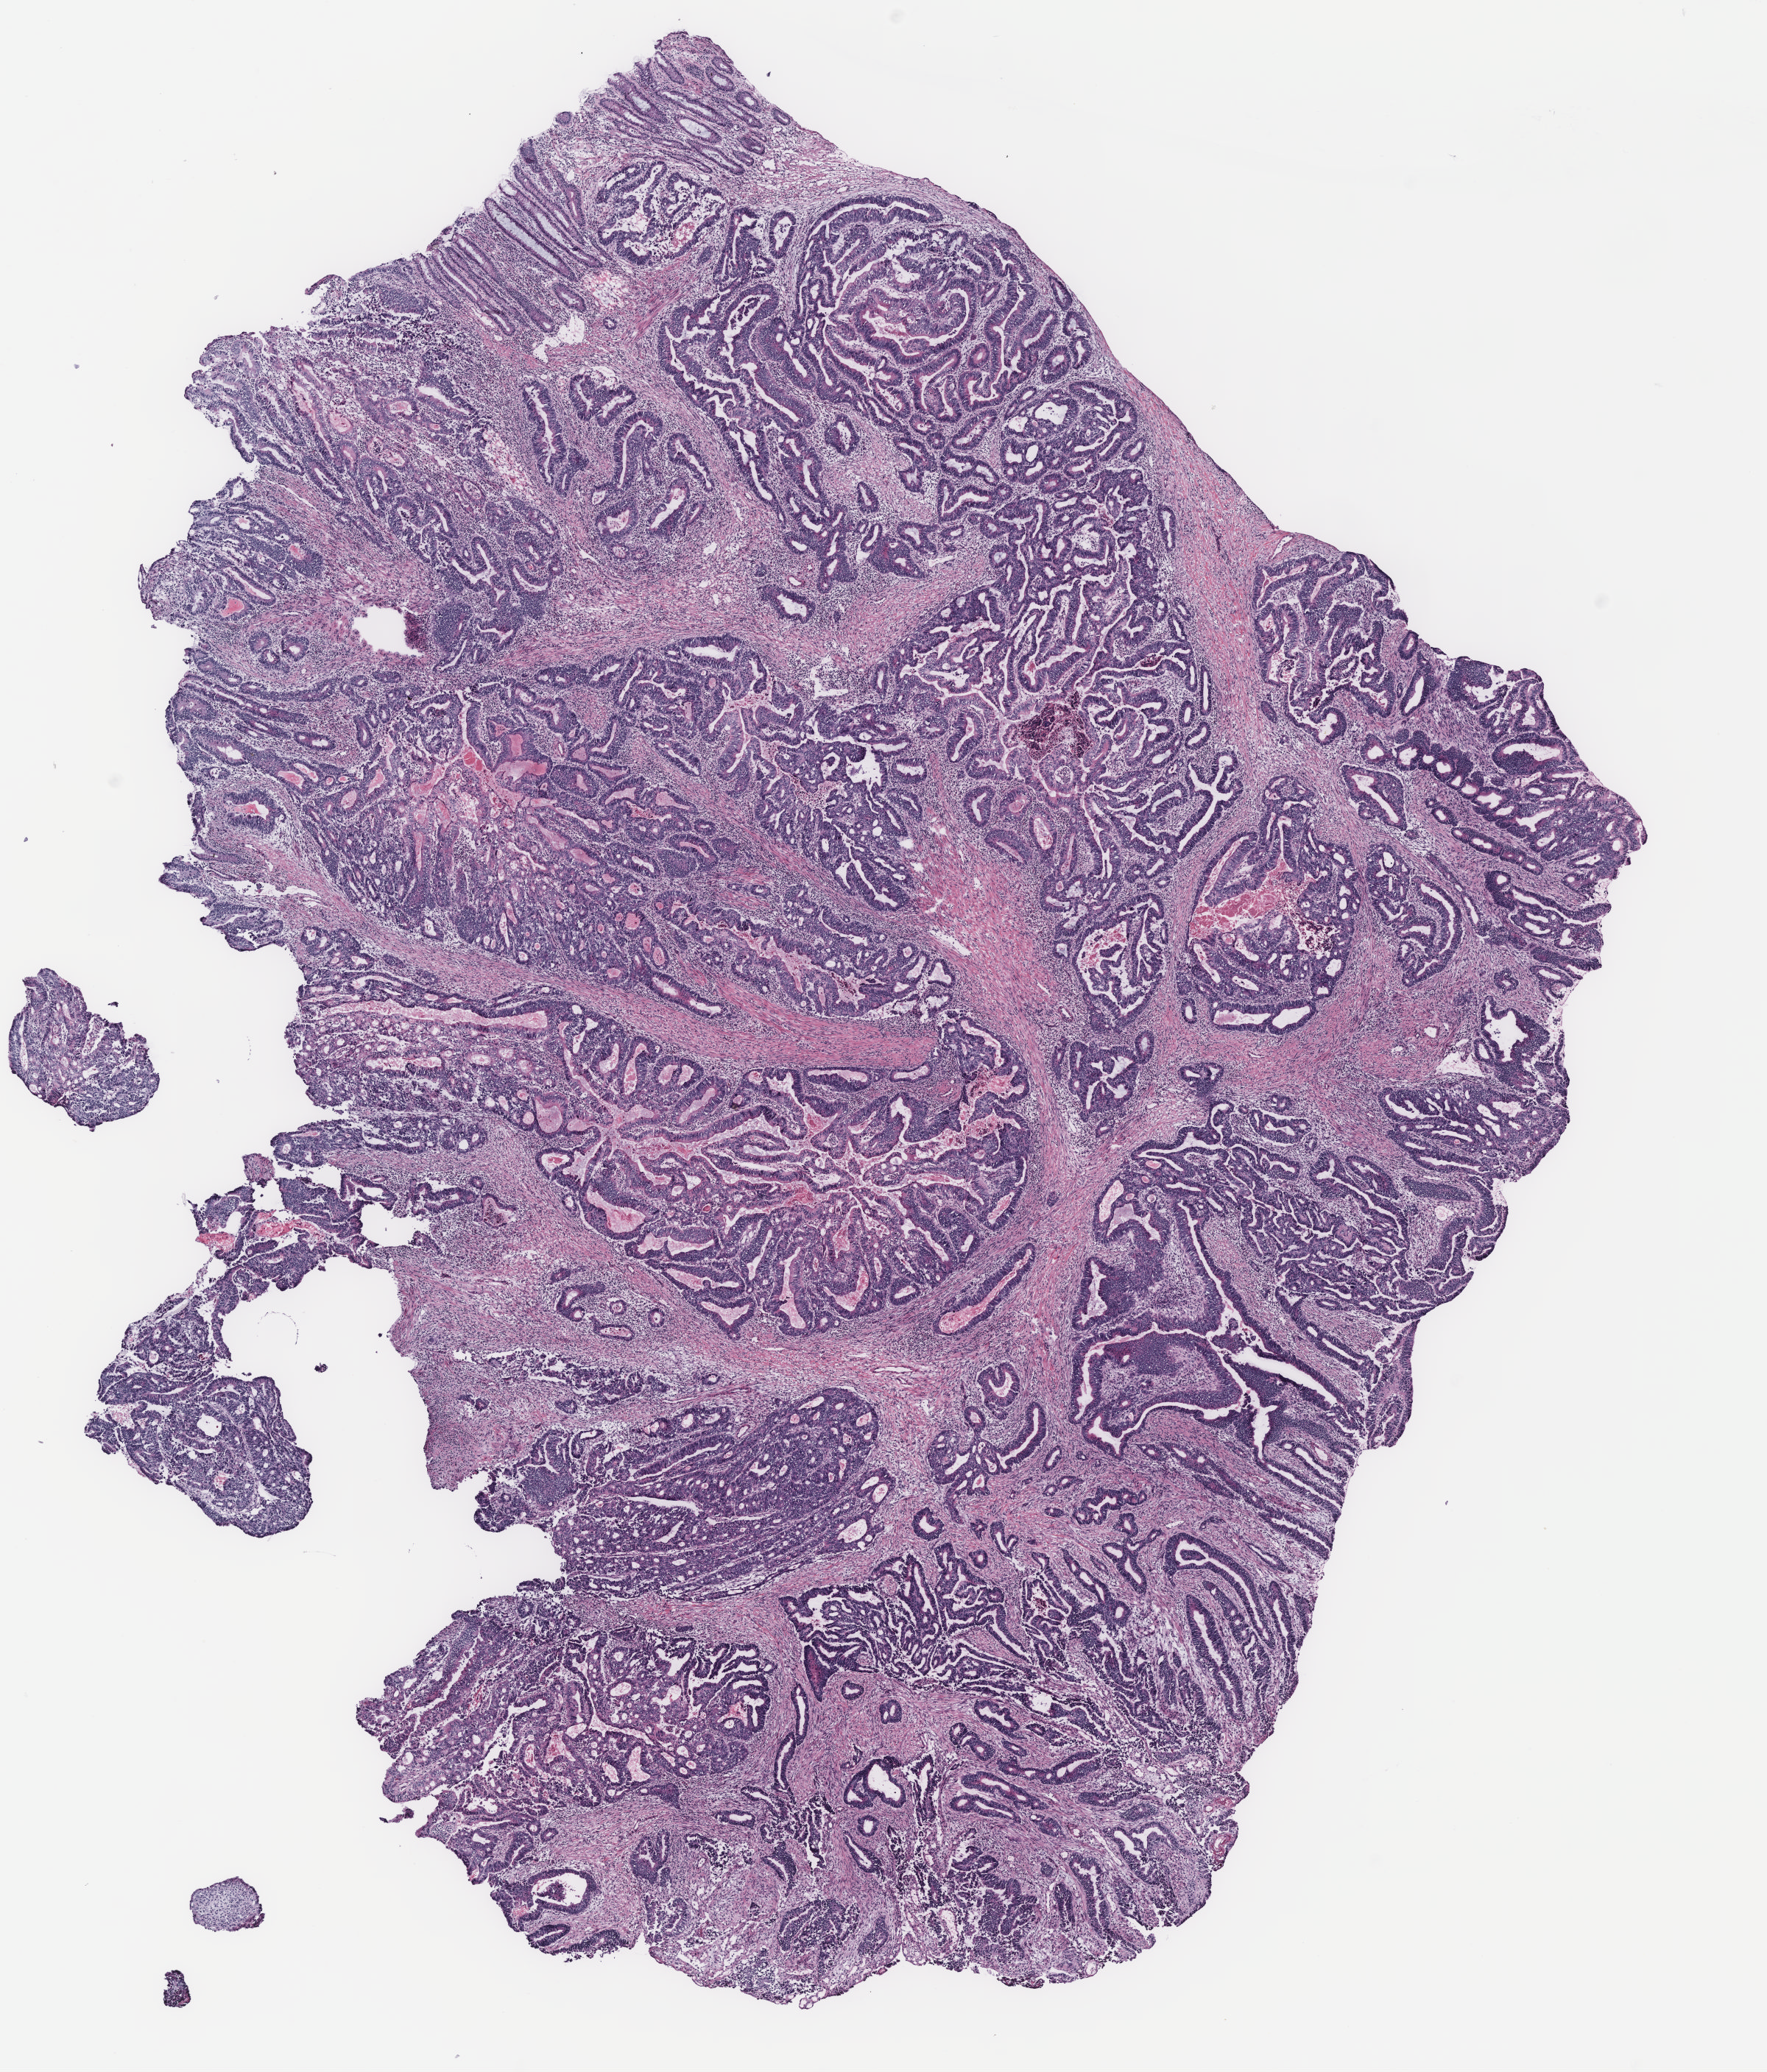
Hematoxylin and eosin (H&E) stained whole-slide image — shown as a low-resolution overview of the whole scanned area (about 9.6 x 11.3 mm, slide scanned at 40x). Colon, tissue type not recorded.
Patient diagnosis (cohort enrolment): colon cancer (colon).